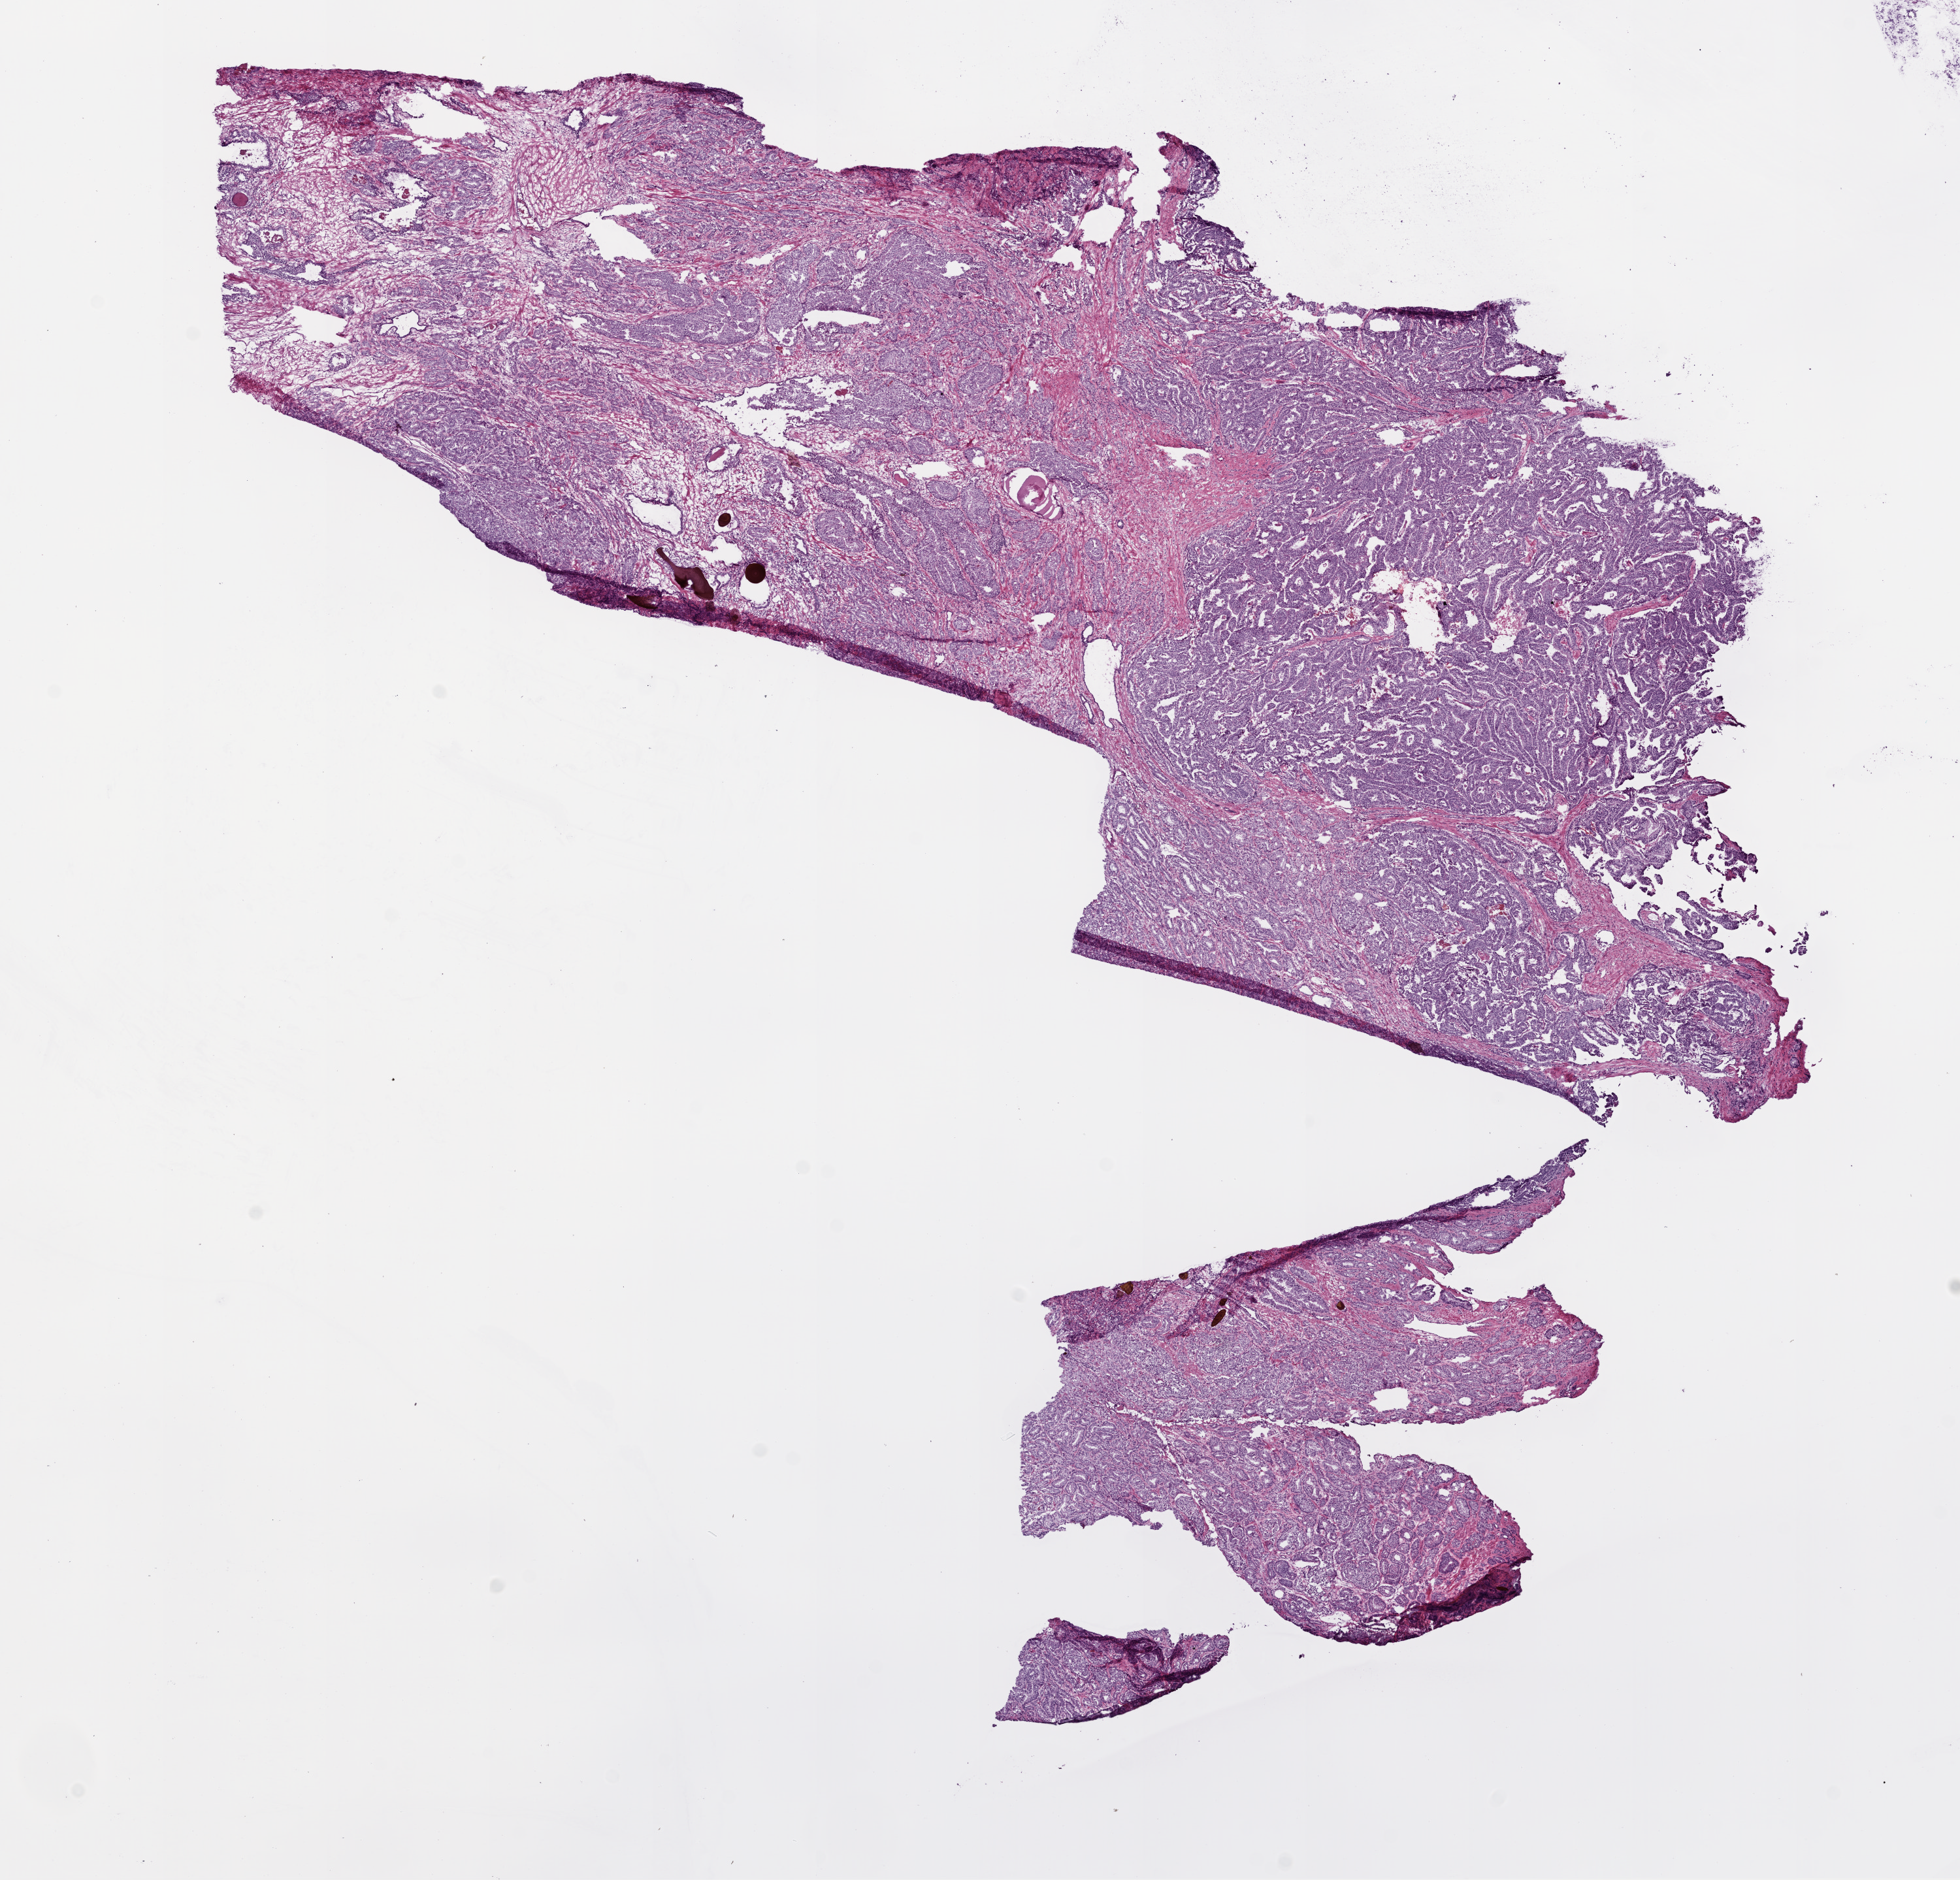
Digitized H&E-stained tissue section (whole slide), shown as a low-resolution overview of the whole scanned area (about 12.0 x 11.5 mm, from a 20x scan). Frozen section. Sample: primary tumour, prostate. Male patient; age at initial diagnosis 62 years. Gleason score: 7 (4+3). Pathologist review of this section (percent, as recorded): tumour cells 70%, tumour nuclei 75%, normal cells 10%, stromal cells 30%, necrosis 0%. Inflammatory infiltration, as recorded: lymphocyte infiltration 3%, monocyte infiltration 2%, neutrophil infiltration 0%.
• lymph nodes positive (case pathology): 0 of 35 examined
• laterality: bilateral
• histologic diagnosis: Acinar cell carcinoma (prostate gland)